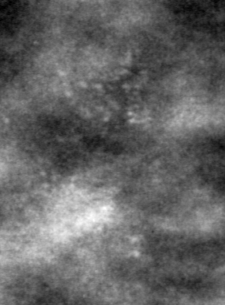
Region of interest cut from a scanned film mammogram (one marked finding); left breast; CC view; BI-RADS breast density category 3 (scale 1–4).
Calcifications, morphology pleomorphic, distribution clustered; BI-RADS assessment category 4; subtlety rating 2 on a 1 (subtle) to 5 (obvious) scale; pathology result (as recorded, not read from the image): malignant.